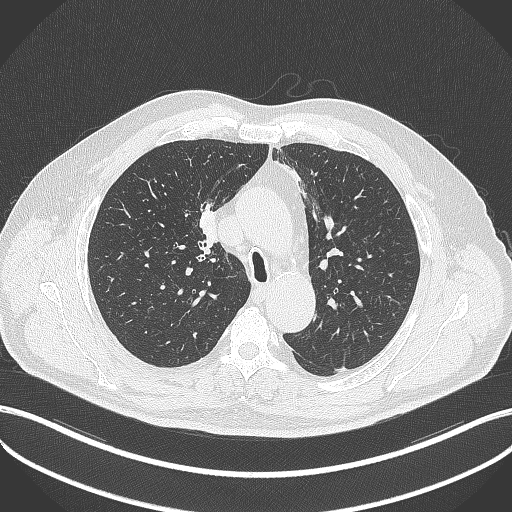
Chest CT, one axial slice; slice 269 of 411 in the series (ordered by position); 120 kVp; lung window (W 1500 / L -600 HU); 1 mm slice thickness; 512 × 512 image matrix, field of view 400 × 400 mm. Male patient, age 60 years. Case-level facts recorded for this patient, not image findings: clinical TNM (as recorded): T1b N1 M0.
Structures marked on this image (bounding box drawn by a radiologist):
- lung tumour (recorded histology: squamous cell carcinoma): bounding box <197,207,222,251> (left, top, right, bottom; pixels)